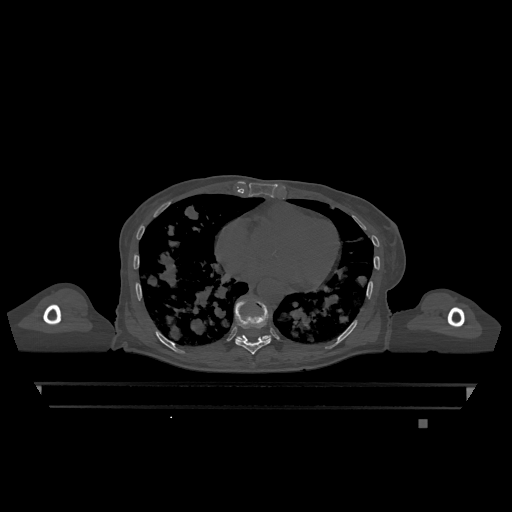
CT including the spine, one axial slice; position 680 of 1317 along the scan axis; bone window (W 1800 / L 400 HU); 512 × 512 image matrix, field of view 500 × 500 mm. Female patient, age 74 years. Case-level facts recorded for this patient, not image findings: primary cancer: lung.
Outlined on this slice (semi-automatic segmentation, software-assisted and operator-edited):
- T10 vertebra: bounding box (x1, y1, x2, y2) in pixels: (235, 335, 271, 341)
- T9 vertebra: (235, 299, 271, 355)